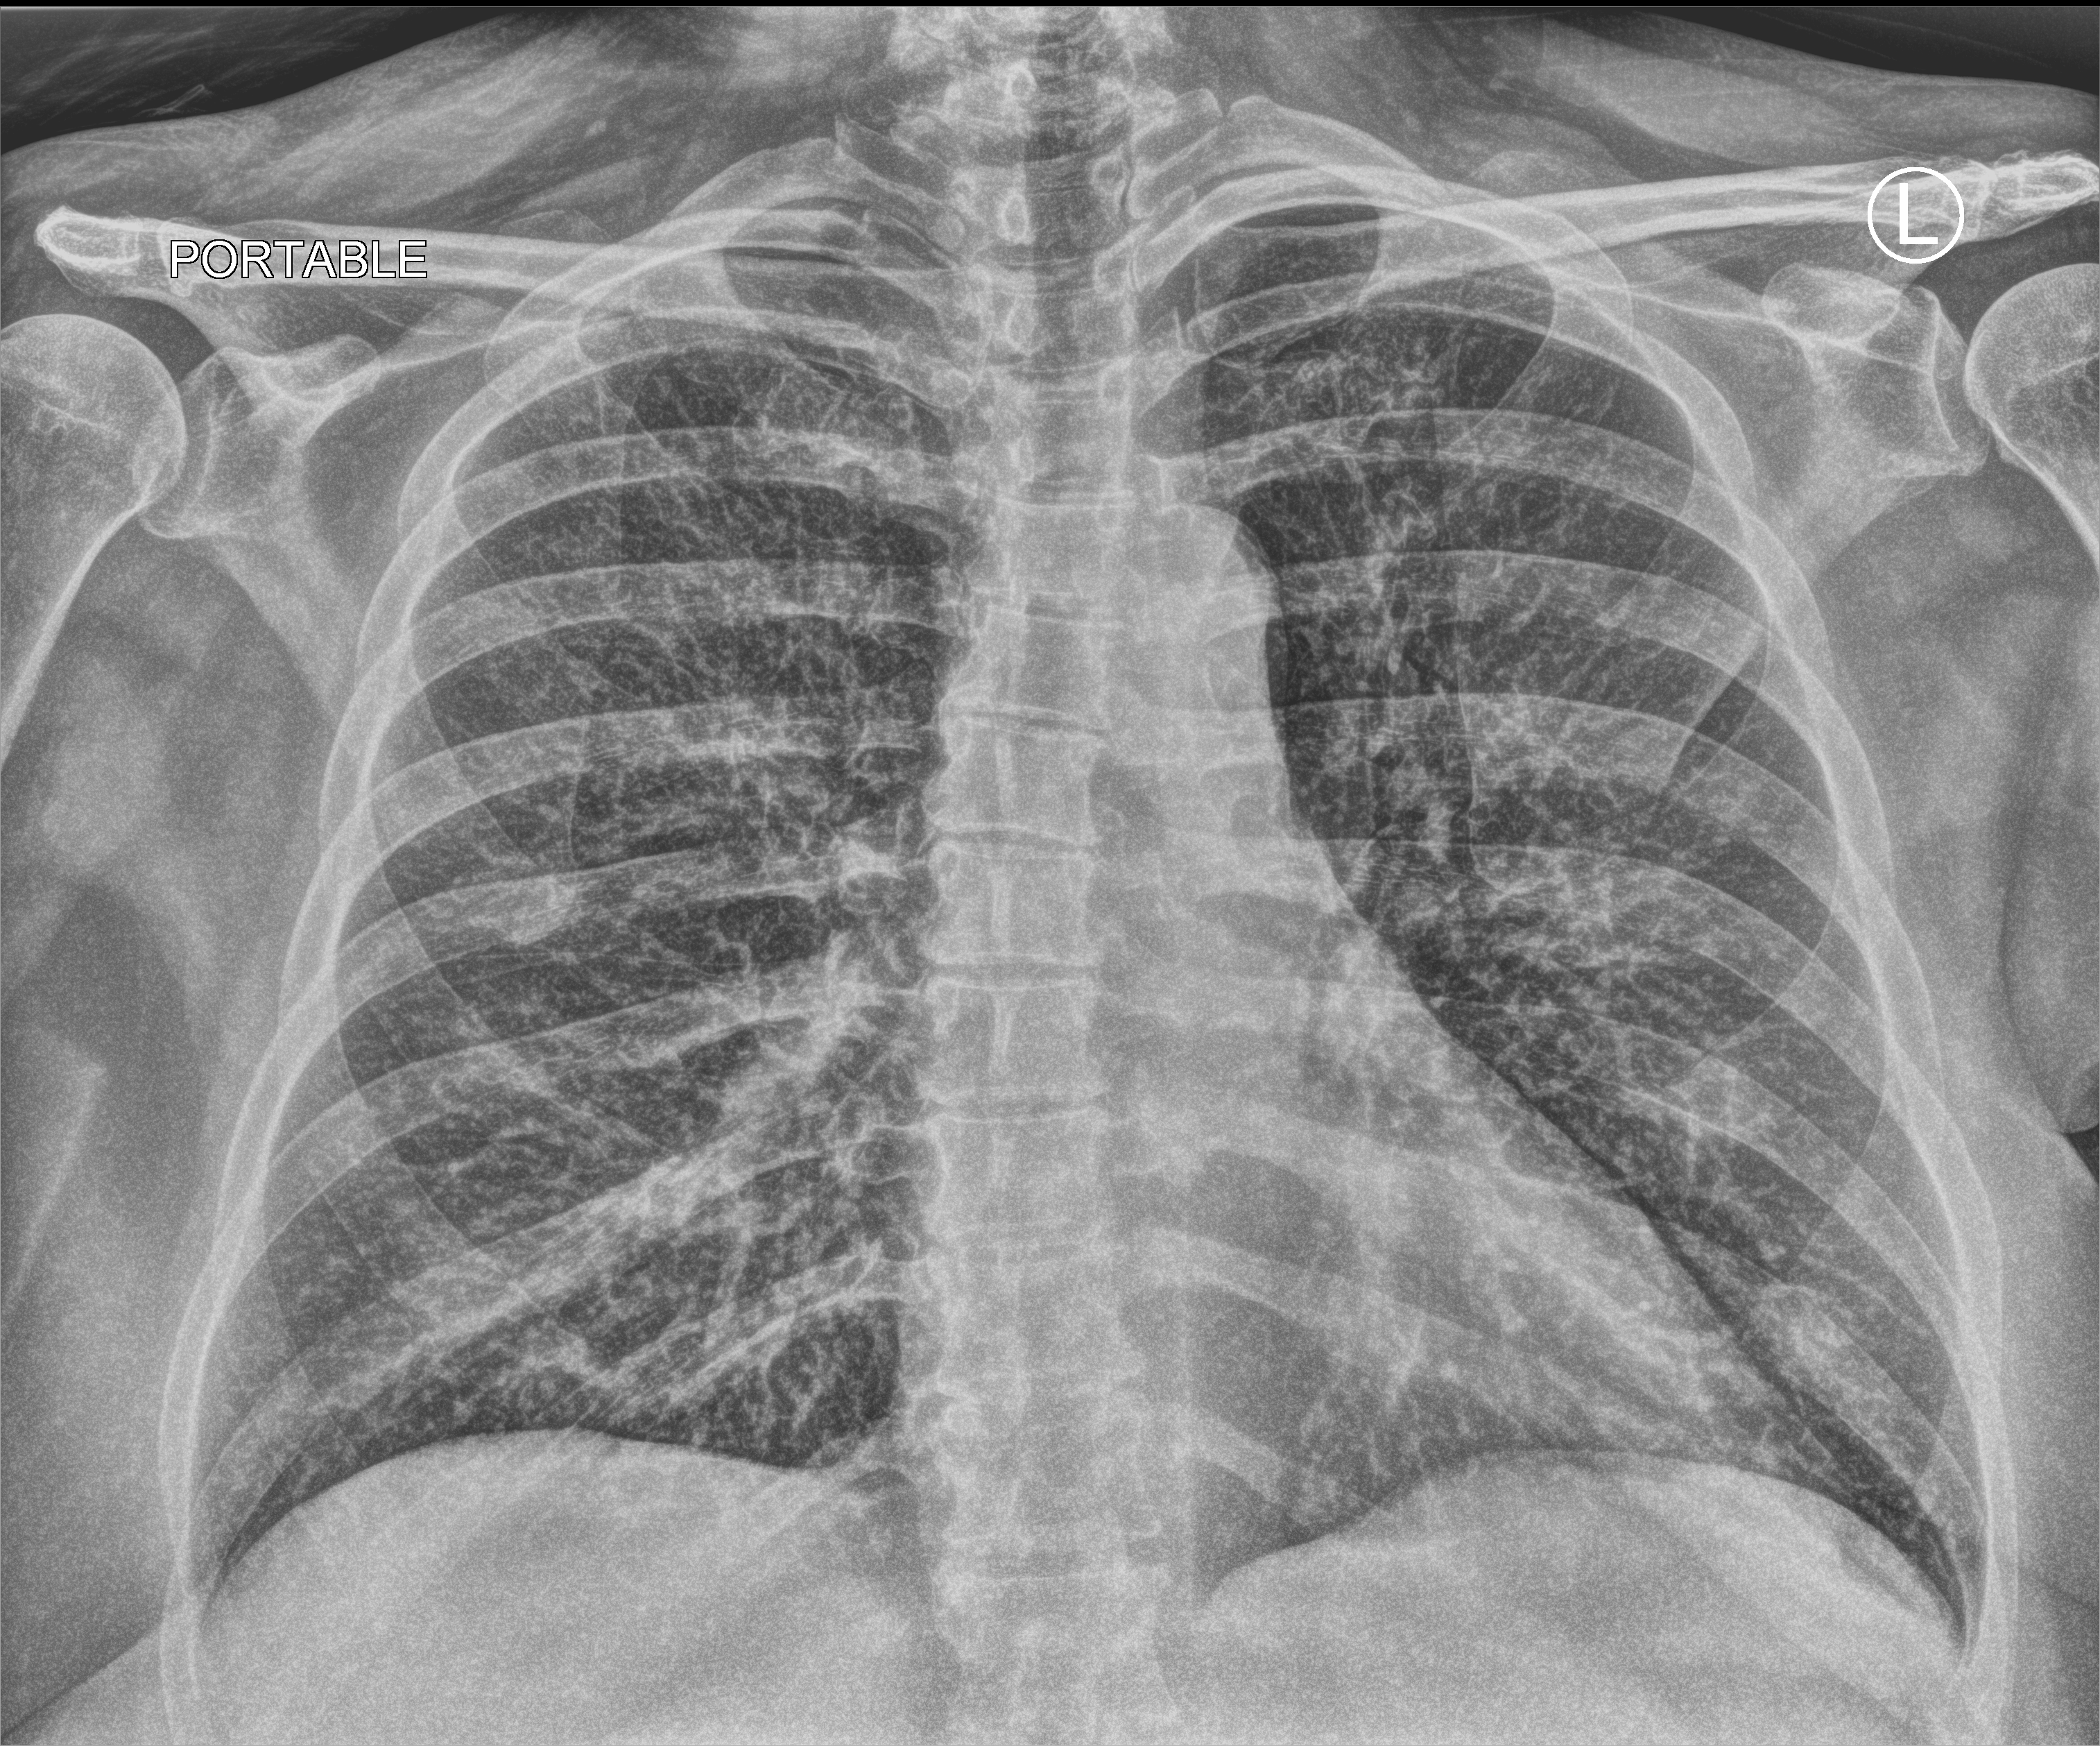
Chest X-ray (portable); anteroposterior (AP) projection. Patient hospitalised with COVID-19; female, aged 18–59 years.
From the hospital-stay record, not from the radiograph (when in the stay this image was taken is not recorded):
- mechanically ventilated during this hospital stay: no